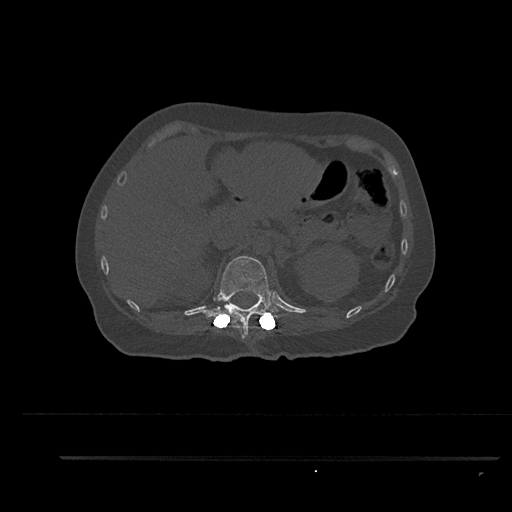
CT including the spine, one axial slice. Slice 258 of 797 in the series (ordered by position). 120 kVp. Bone window (W 1800 / L 400 HU). 0.5 mm slice thickness. 512 × 512 image matrix, field of view 408 × 408 mm. Female patient, age 44 years. Case-level facts recorded for this patient, not image findings: primary cancer: renal.
Outlined on this slice (semi-automatic segmentation, software-assisted and operator-edited):
- T12 vertebra: box from (x=204, y=256) to (x=278, y=339) px